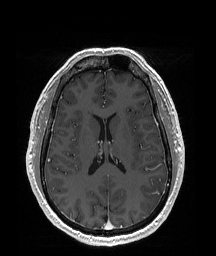
Brain MRI from a brain-tumour surgery series, one axial slice; position 86 of 192 along the scan axis; T1-weighted post-contrast; 1 mm slice thickness; 216 × 256 image matrix. Case-level facts recorded for this patient, not image findings: histopathology: Glioblastoma; WHO grade: 4; IDH mutation: no; tumour location: Left Temporal Parietal.
Structures marked on this image (manually delineated by an expert):
- tumour: bounding box (x1, y1, x2, y2) in pixels: (141, 178, 166, 211)